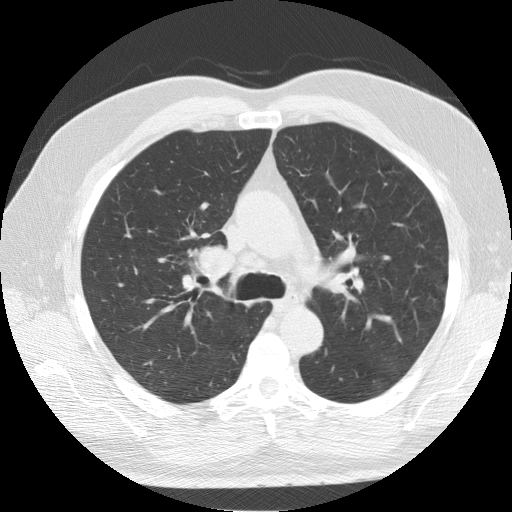
Axial slice from a low-dose chest CT screening exam; second screening round (one year after baseline); lung window (W 1500 / L -600 HU); 2.5 mm slice thickness; 512 × 512 image matrix. Male participant, aged 64 years at enrolment.
Expert reader's lesion annotation, bounding box (x1, y1, x2, y2) in pixels: (173, 227, 252, 304). The exam's reader record, not a measurement of the box and not confirmed to be the same lesion: non-calcified nodule or mass ≥4 mm, right lower lobe, 7 × 5 mm, smooth margins, soft tissue attenuation, pre-existing on the prior screen: yes; interval growth: no.